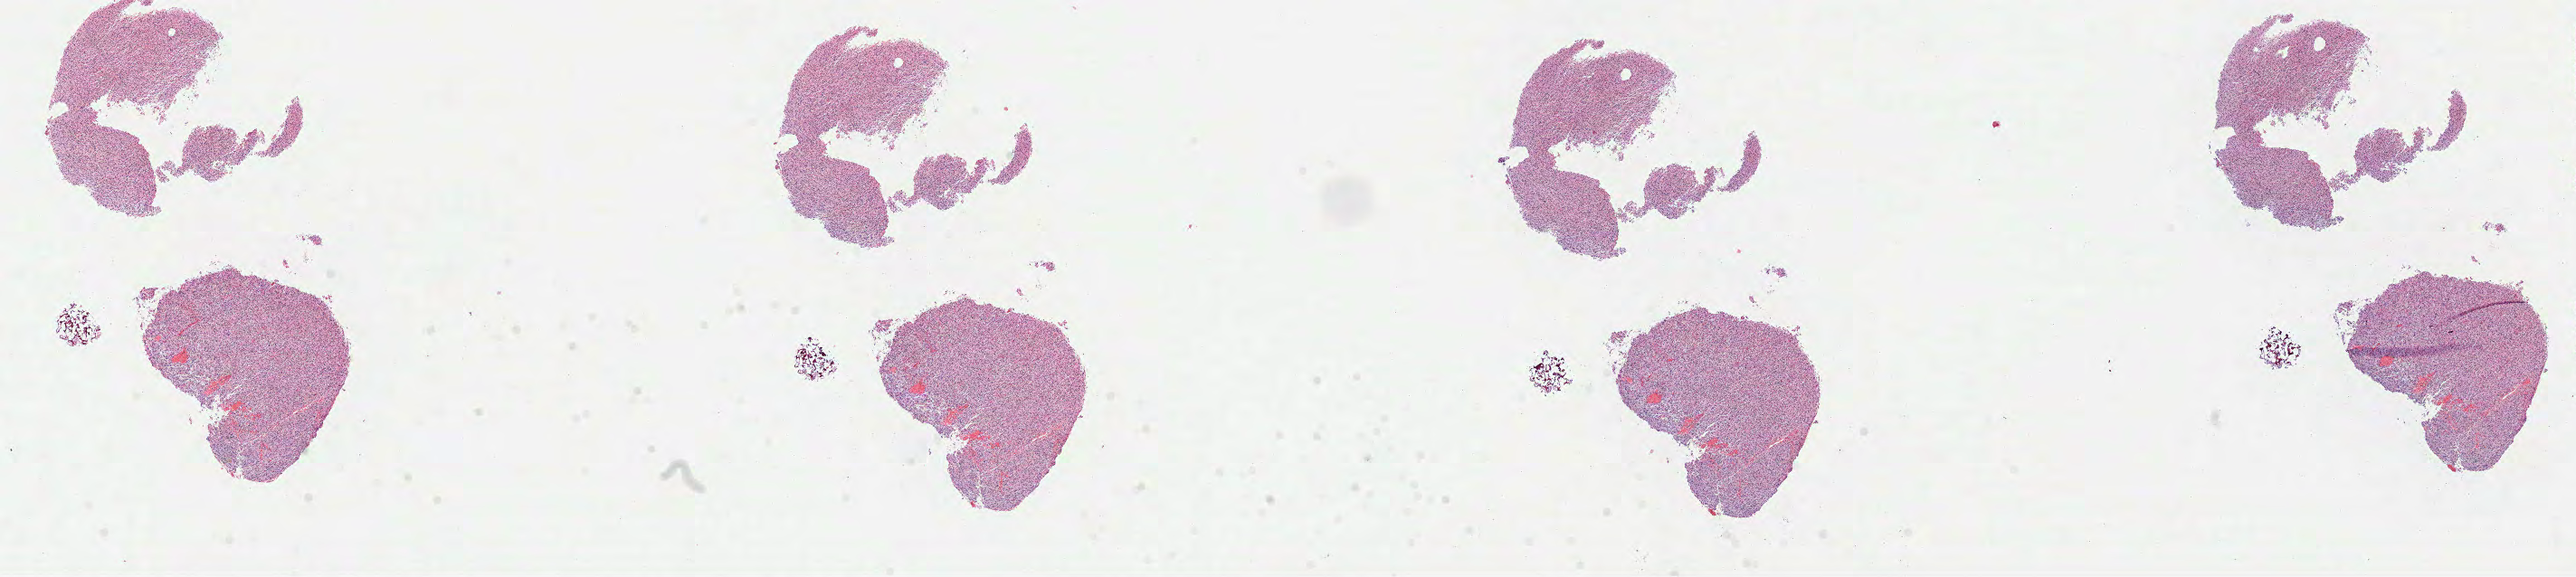
Digitized Hematoxylin and eosin (H&E) stained tissue section (whole slide) — whole scanned area (about 23.0 x 5.1 mm, acquisition: 40x scan) shown as a low-resolution overview. FFPE section. Sample: primary tumour, brain. Female patient; age at initial diagnosis 40 years.
Histologic diagnosis: Mixed glioma.